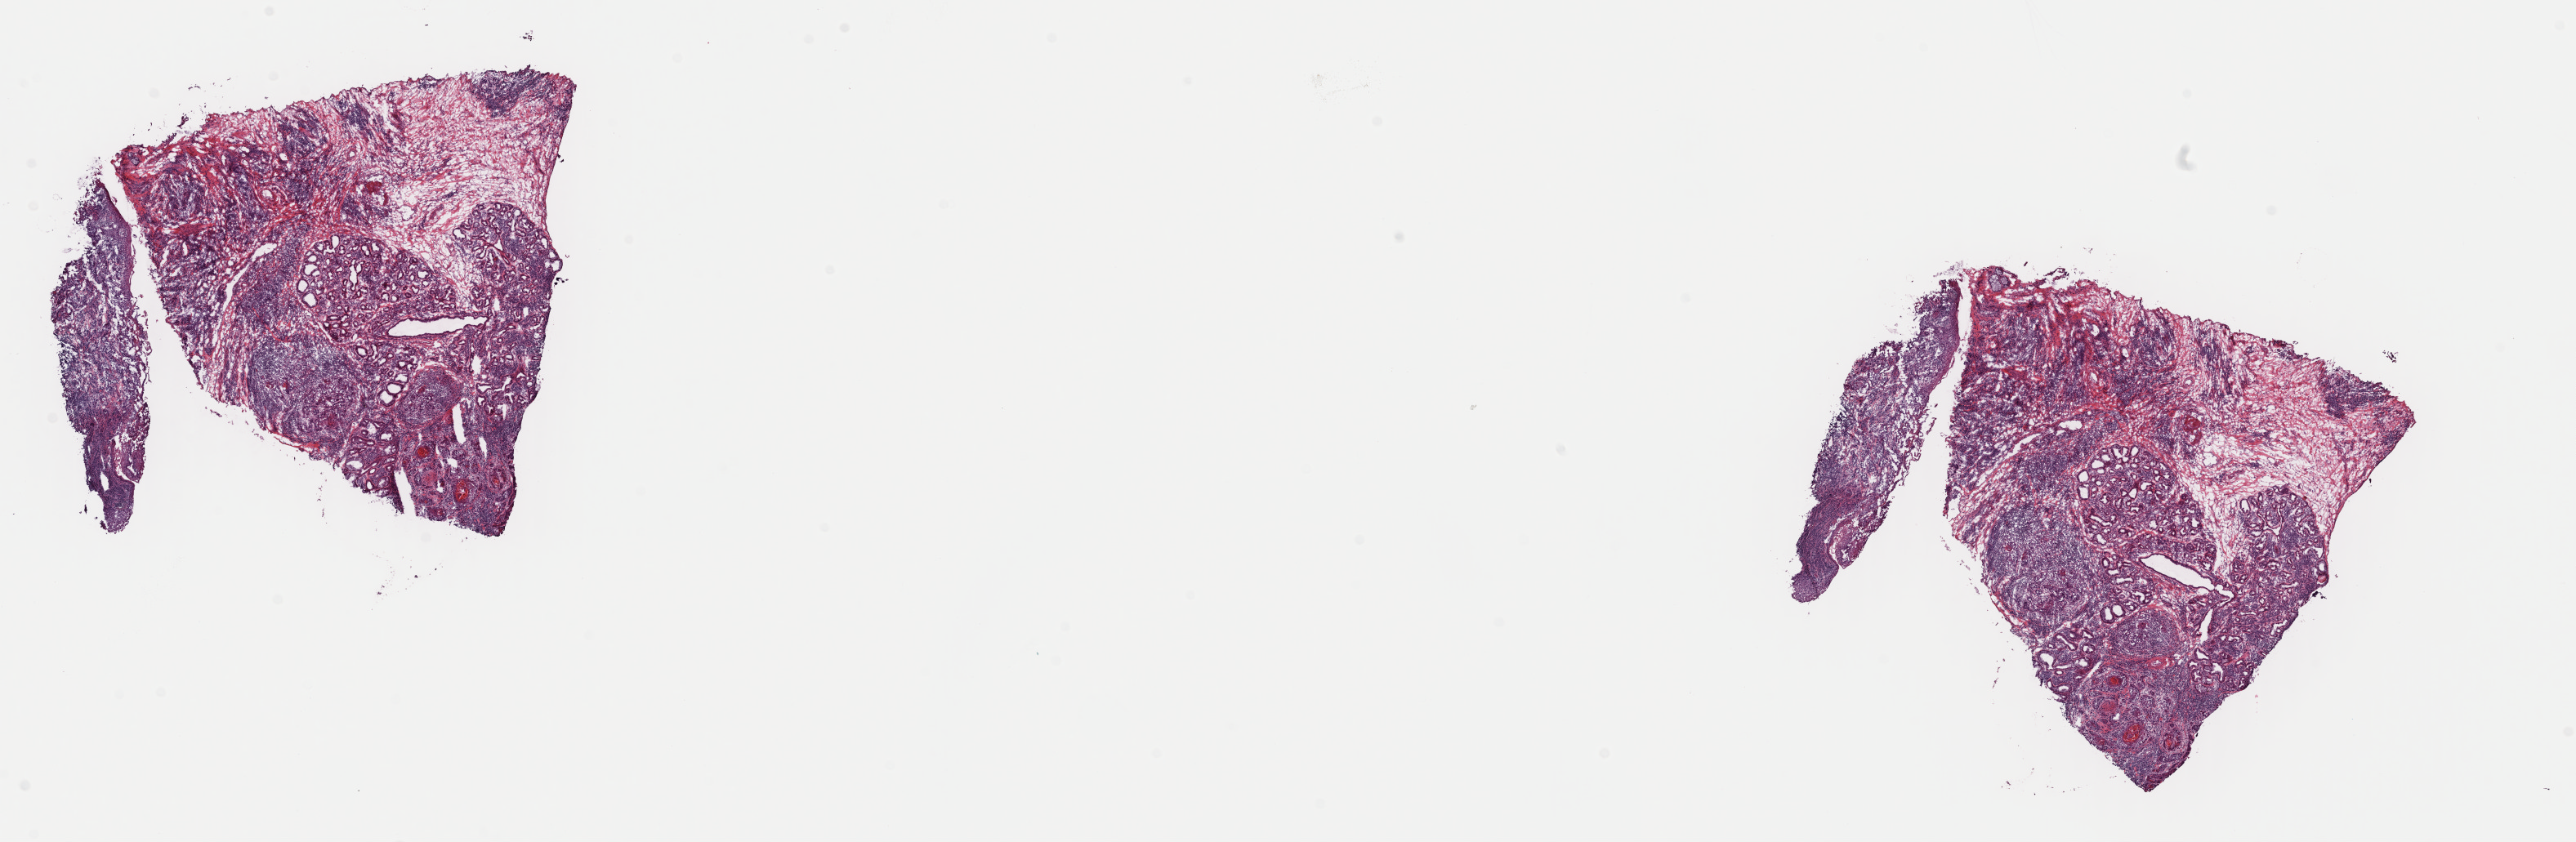
H&E-stained whole-slide image, low-resolution overview of the scanned area, about 24.9 x 8.1 mm; frozen section from the top of the tissue portion; primary tumour sample from the head and neck. Male, age 60 years at initial diagnosis. Histologic grade: G3 (poorly differentiated). Slide review estimates, as recorded: tumour cells 60%, tumour nuclei 60%, normal cells 0%, stromal cells 40%, necrosis 0%. Inflammatory infiltration, as recorded: lymphocyte infiltration 30%, monocyte infiltration 20%, neutrophil infiltration 30%.
Diagnosis: Squamous cell carcinoma, NOS (larynx, NOS). AJCC pathologic stage: IVA (7th edition). Lymph nodes positive (case pathology): 0 of 80 examined.